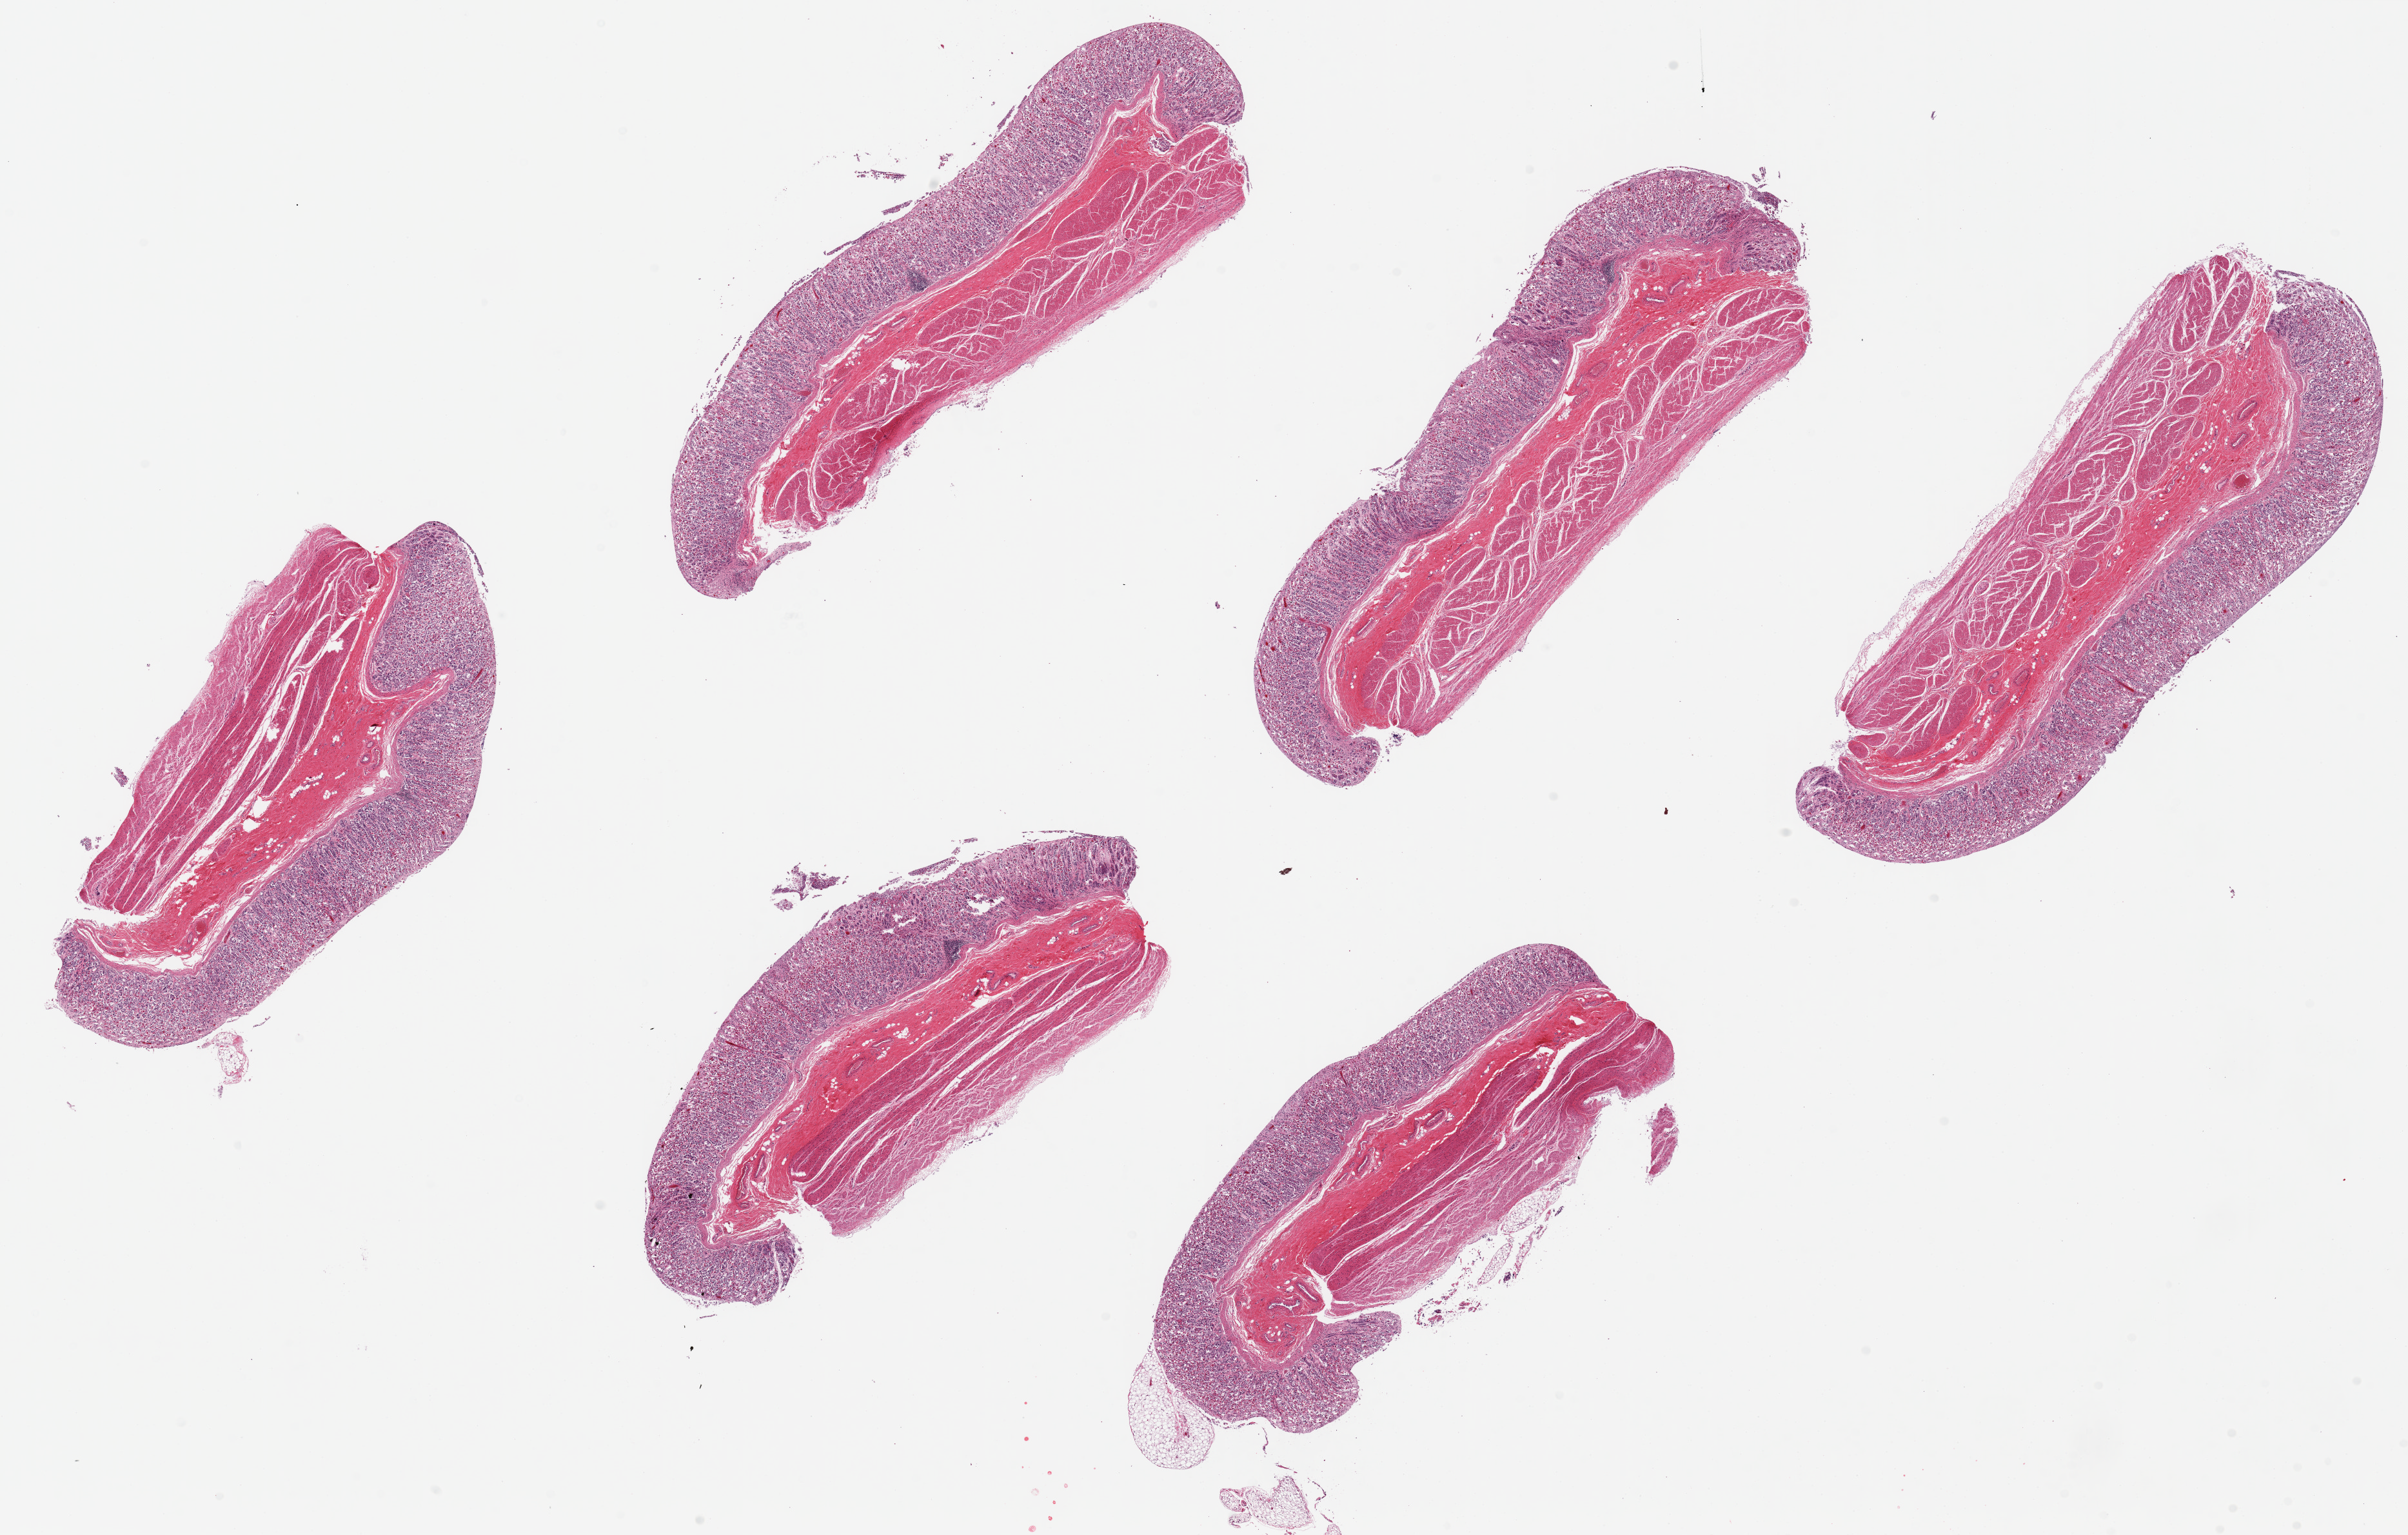
Whole-slide image, haematoxylin and eosin stain, shown as a low-resolution overview of the whole scanned area (about 29.5 x 18.8 mm, from a 20x scan); PAXgene-fixed, paraffin-embedded tissue; section of stomach (target tissue); tissue donor sample. Donor sex: male.
Review note (as recorded): 6 pieces ~8x2mm. Muscosa moderately autolyzed, ~3-40% of thickness.